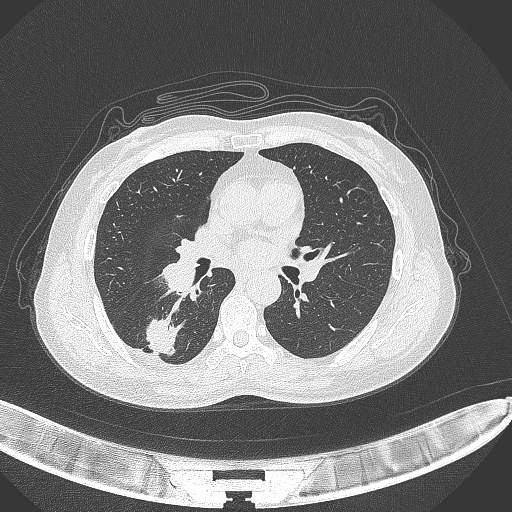
Chest CT, one axial slice. Slice 162 of 352 in the series (ordered by position). 120 kVp. Lung window (W 1500 / L -600 HU). 1 mm slice thickness. 512 × 512 image matrix, field of view 400 × 400 mm. Female patient, age 55 years. From the clinical record (not read from this slice): clinical TNM (as recorded): T1c N1 M0.
Annotated regions visible in this slice (rectangle marked by the reading radiologist):
- lung tumour (recorded histology: adenocarcinoma): bounding box <143,313,180,358> (left, top, right, bottom; pixels)